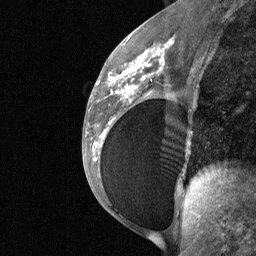
Breast MRI (dynamic contrast-enhanced), one sagittal slice. Slice 34 of 64 in the series (ordered by position). Dynamic contrast-enhanced study with each time point stored as its own series, time point 2 of 3 at this slice position (early post-contrast, ordered by acquisition time). 1.5 T. TE 4.8 ms, TR 27 ms. 2 mm slice thickness. 256 × 256 image matrix. Female patient, age 34 years. Case-level facts recorded for this patient, not image findings: setting: breast cancer imaged before/during neoadjuvant chemotherapy; receptor status: HR-positive, HER2-negative.
Outlined on this slice (semi-automatically segmented with operator editing):
- analysis volume of interest (the breast-tissue region the enhancement analysis was run in; not a lesion): bounding box [x1, y1, x2, y2] px = [92, 50, 188, 185]
- tumour enhancement mask (voxels above the 90 % enhancement threshold inside the analysis volume of interest): [108, 50, 162, 124]